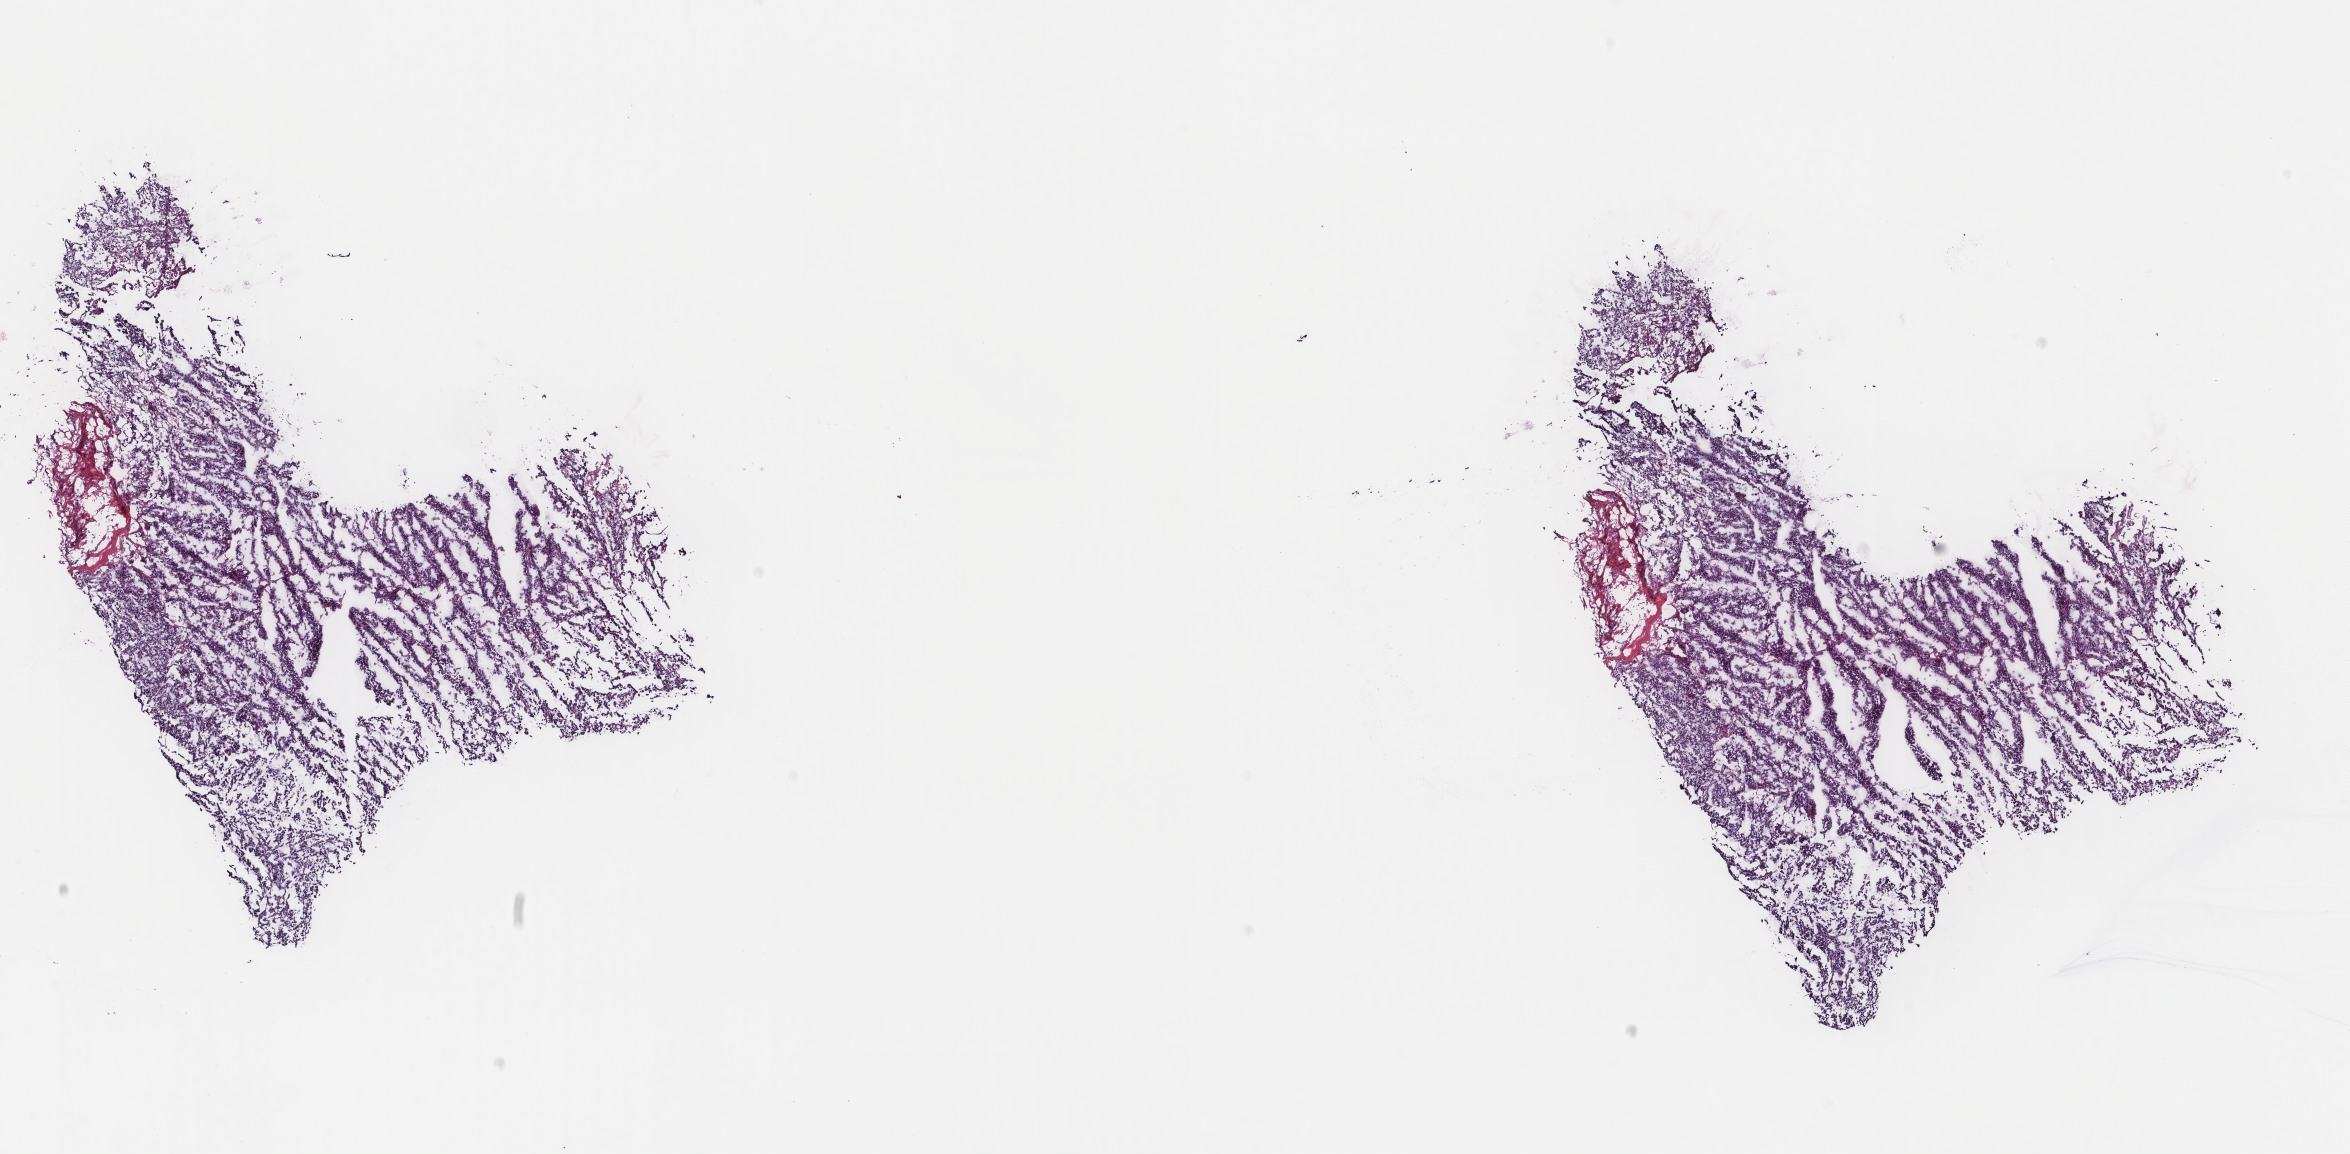
Digitized H&E tissue section (whole slide) — whole scanned area (about 18.7 x 9.2 mm, slide scanned at 40x) shown as a low-resolution overview; frozen section from the top of the tissue portion; metastatic tumour sample. Female patient; age at initial diagnosis 79 years. Slide review estimates, as recorded: tumour cells 85%, tumour nuclei 85%, normal cells 0%, stromal cells 14%, necrosis 1%. Infiltration values recorded for this section: lymphocyte infiltration 2%, monocyte infiltration 2%, neutrophil infiltration 1%.
This section: metastatic tumour tissue. Patient diagnosis: Malignant melanoma, NOS.